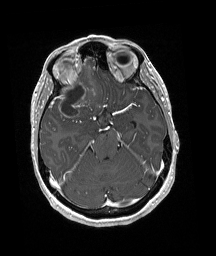
Brain MRI from a brain-tumour surgery series, one axial slice. Position 122 of 192 along the scan axis. T1-weighted post-contrast. 1 mm slice thickness. 216 × 256 image matrix. From the clinical record (not read from this slice): histopathology: Oligodendroglioma; WHO grade: 3; IDH mutation: yes; tumour location: Right Frontal.
Annotated regions visible in this slice (expert manual segmentation):
- tumour: box from (x=51, y=74) to (x=96, y=119) px